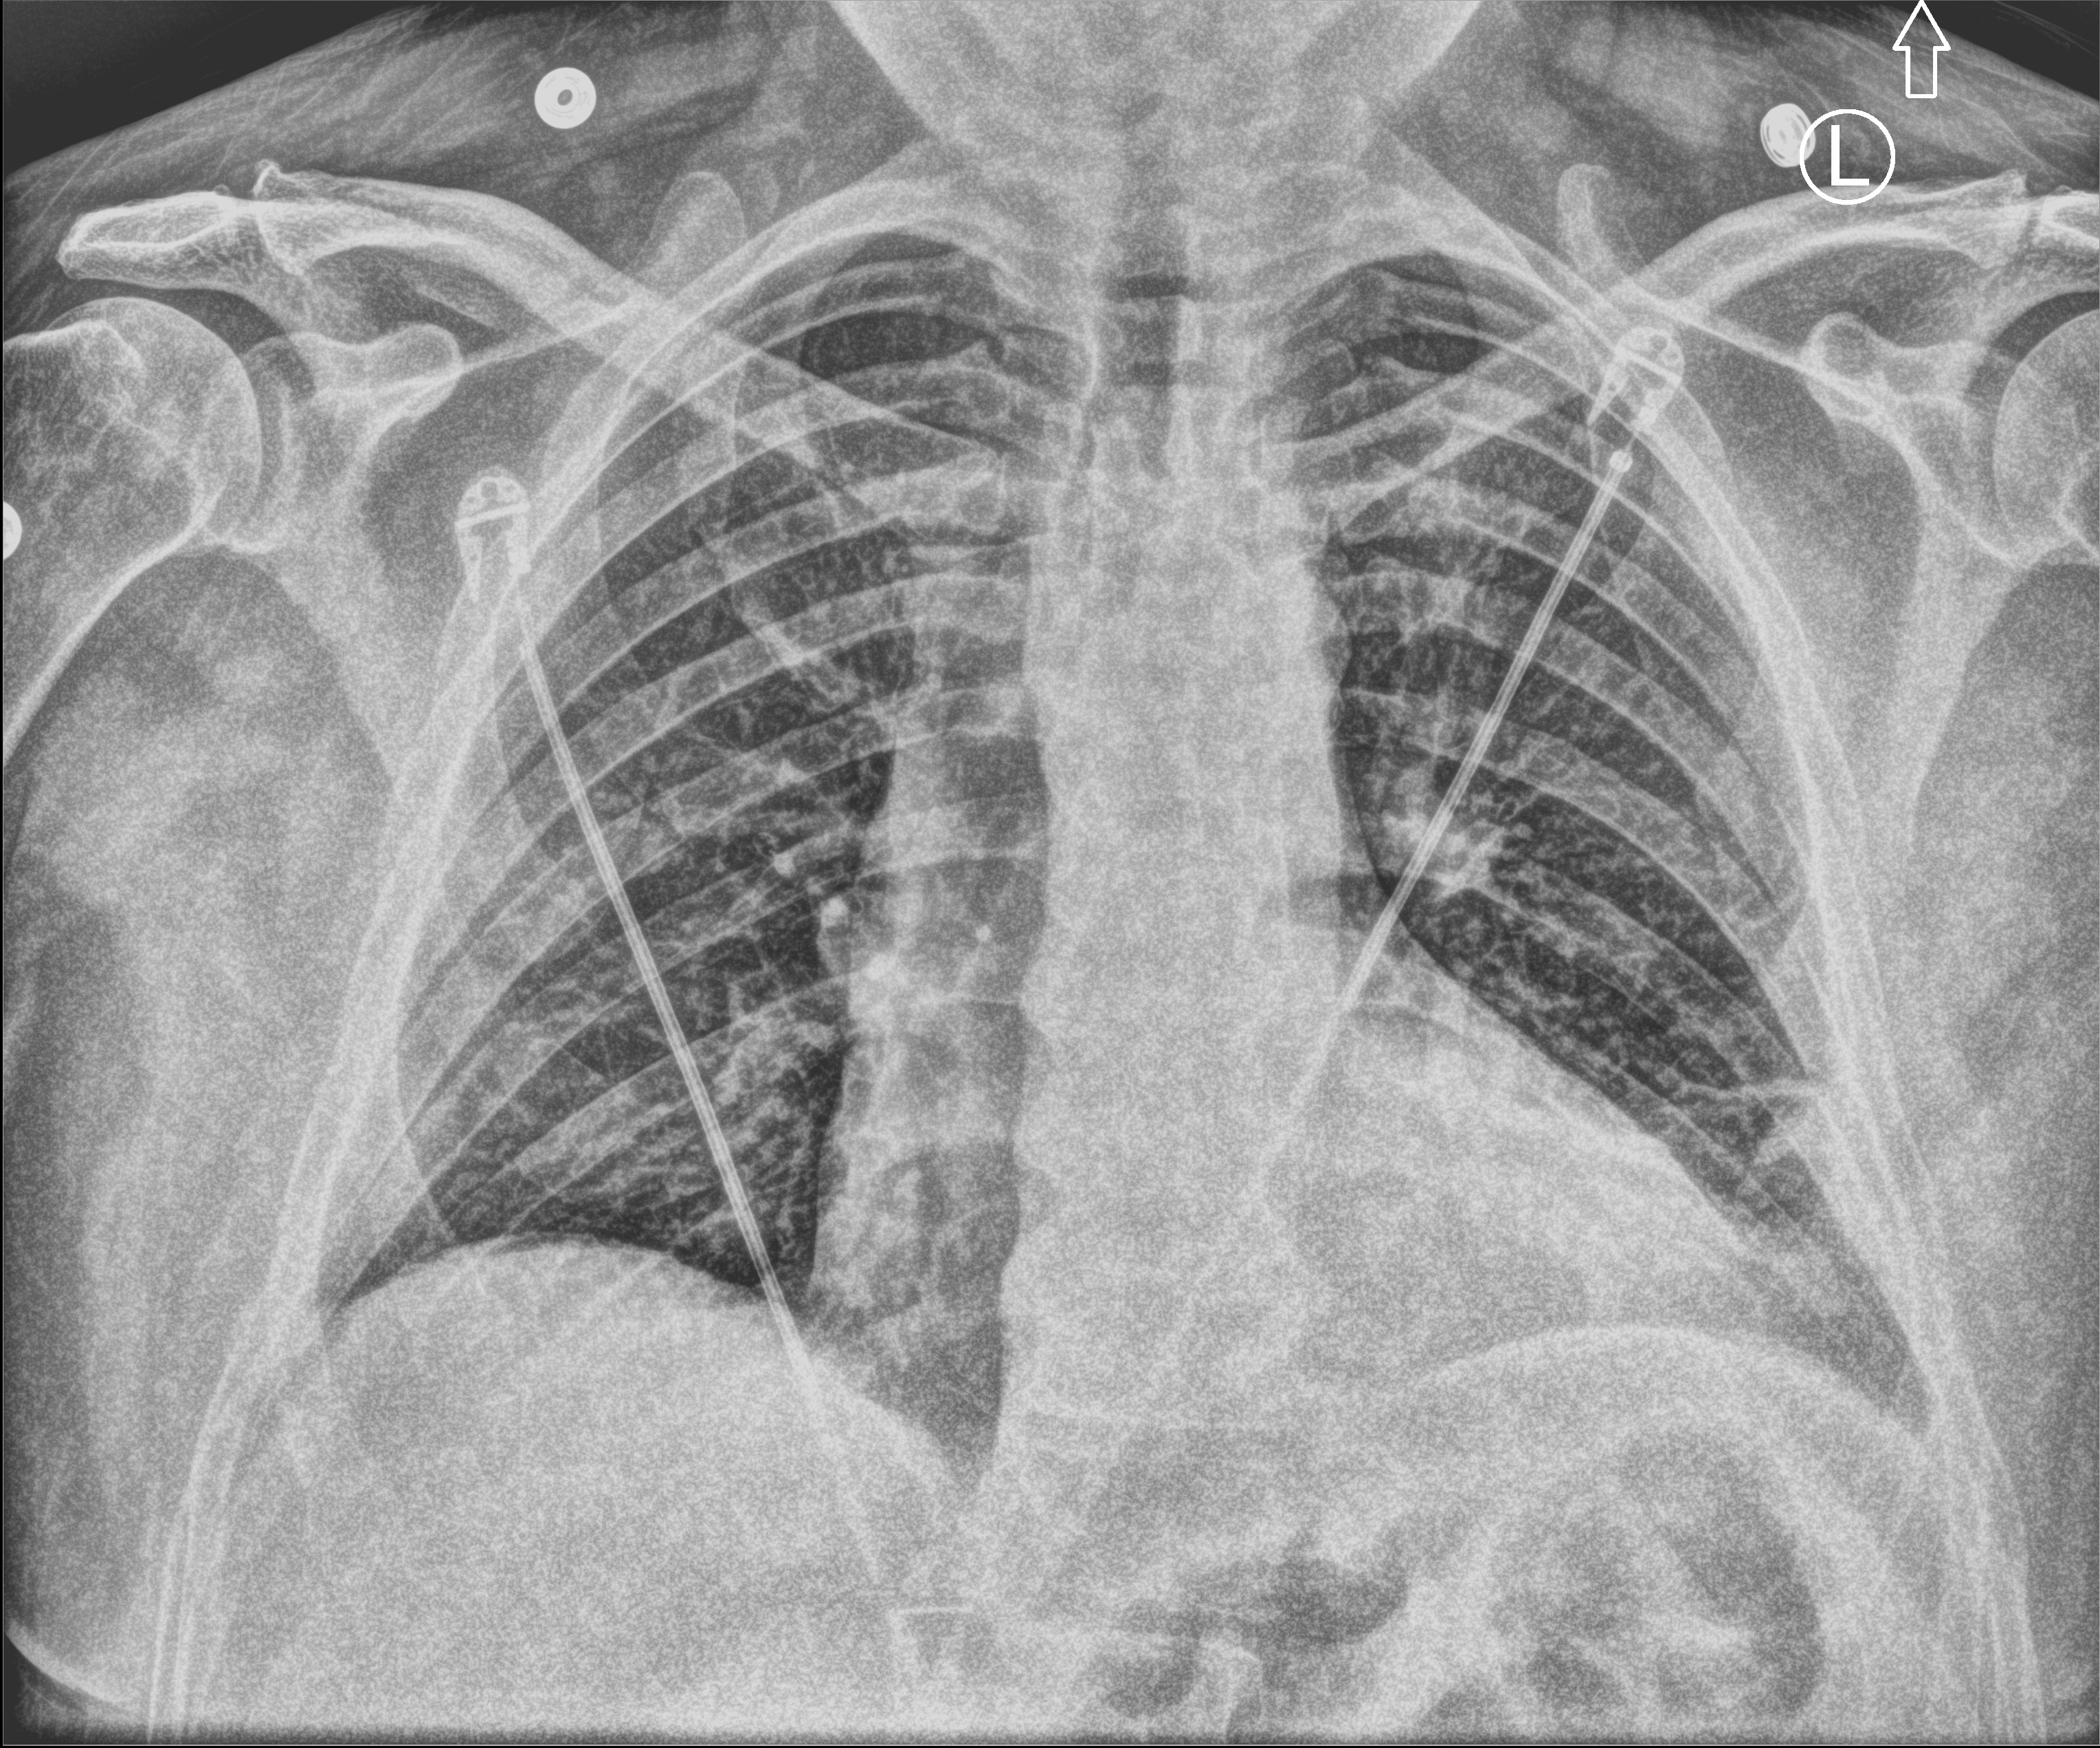
Bedside chest radiograph (computed radiography), anteroposterior (AP) projection. Male patient hospitalised with COVID-19, age 18–59 years.
Hospital-stay facts (about this admission, not read from this image; timing relative to this image not recorded):
- admitted to intensive care during this hospital stay: no